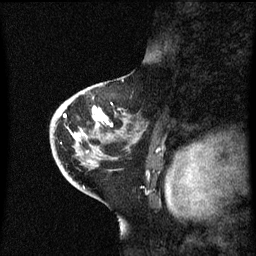
Breast MRI (dynamic contrast-enhanced), one sagittal slice. Slice 37 of 60 in the series (ordered by position). Dynamic contrast-enhanced series, image 2 of 3 at this slice position (ordered by acquisition). 1.5 T. TE 4.2 ms, TR 8.4 ms. 2.3 mm slice thickness. 256 × 256 image matrix, field of view 200 × 200 mm. Patient: female, 46 years. From the clinical record (not read from this slice): setting: breast cancer imaged before/during neoadjuvant chemotherapy; receptor status: HER2-positive.
Structures marked on this image (semi-automatic segmentation, software-assisted and operator-edited):
- analysis volume of interest (the breast-tissue region the enhancement analysis was run in; not a lesion): bounding box [x1, y1, x2, y2] px = [50, 86, 141, 171]
- tumour enhancement mask (voxels above the 70 % enhancement threshold inside the analysis volume of interest): [64, 106, 107, 141]